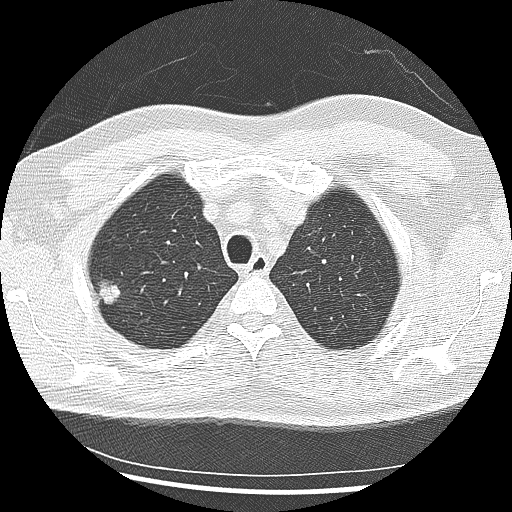
Low-dose screening chest CT, one axial slice; reconstruction kernel LUNG; 120 kVp; lung window (W 1500 / L -600 HU); 2.5 mm slice thickness; 512 × 512 image matrix.
Structures marked on this image (expert manual segmentation):
- lesion 1 (tumor, upper lobe of right lung): bounding box [x1, y1, x2, y2] px = [100, 283, 120, 304]